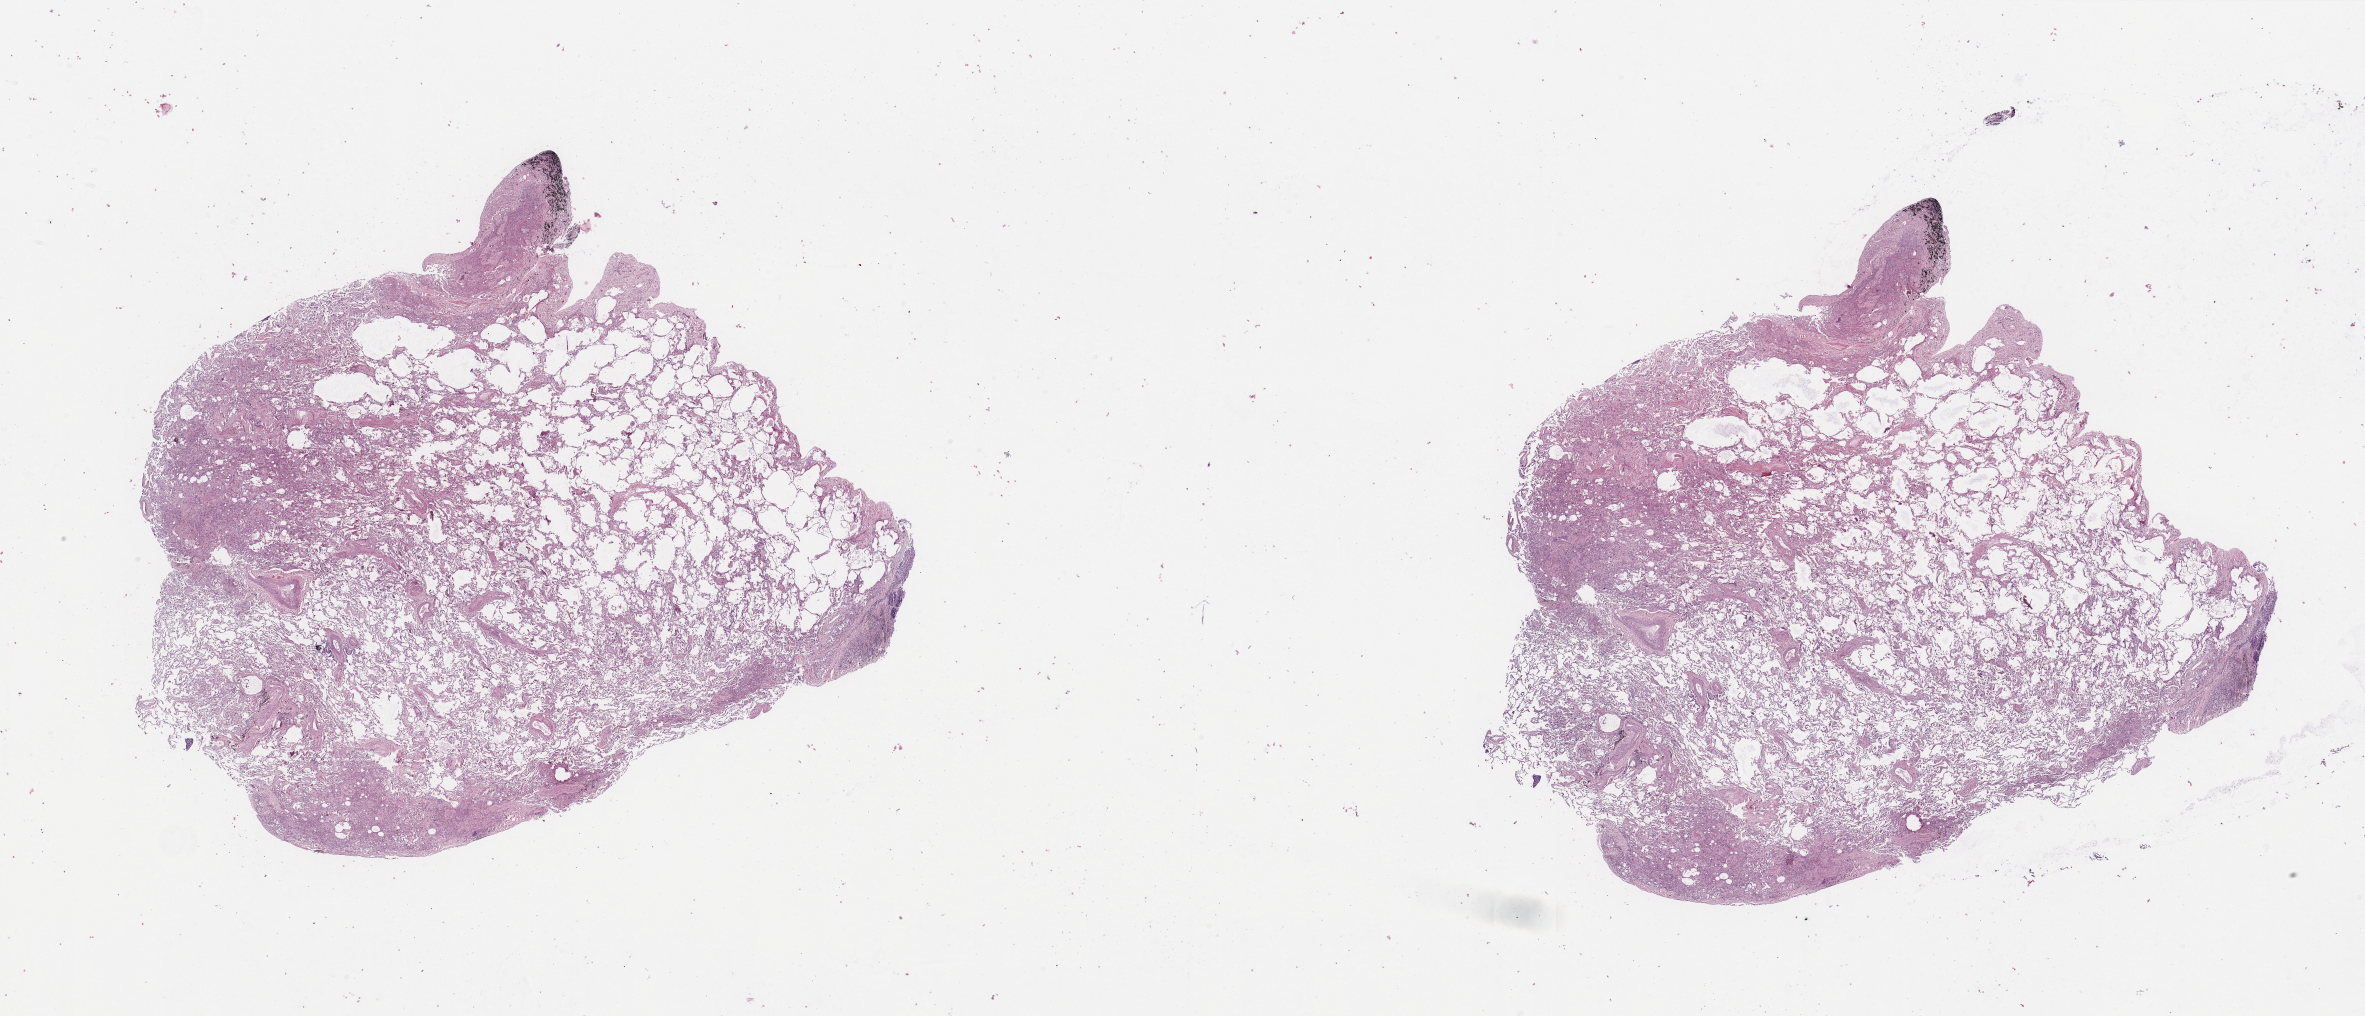
H&E whole-slide image — shown as a low-resolution overview of the whole scanned area (about 37.4 x 16.1 mm), normal (non-tumour) tissue sample, sampled site: lung. 61-year-old male patient.
This section: normal (non-tumour) tissue from the same patient. Patient diagnosis: Squamous cell carcinoma, NOS.